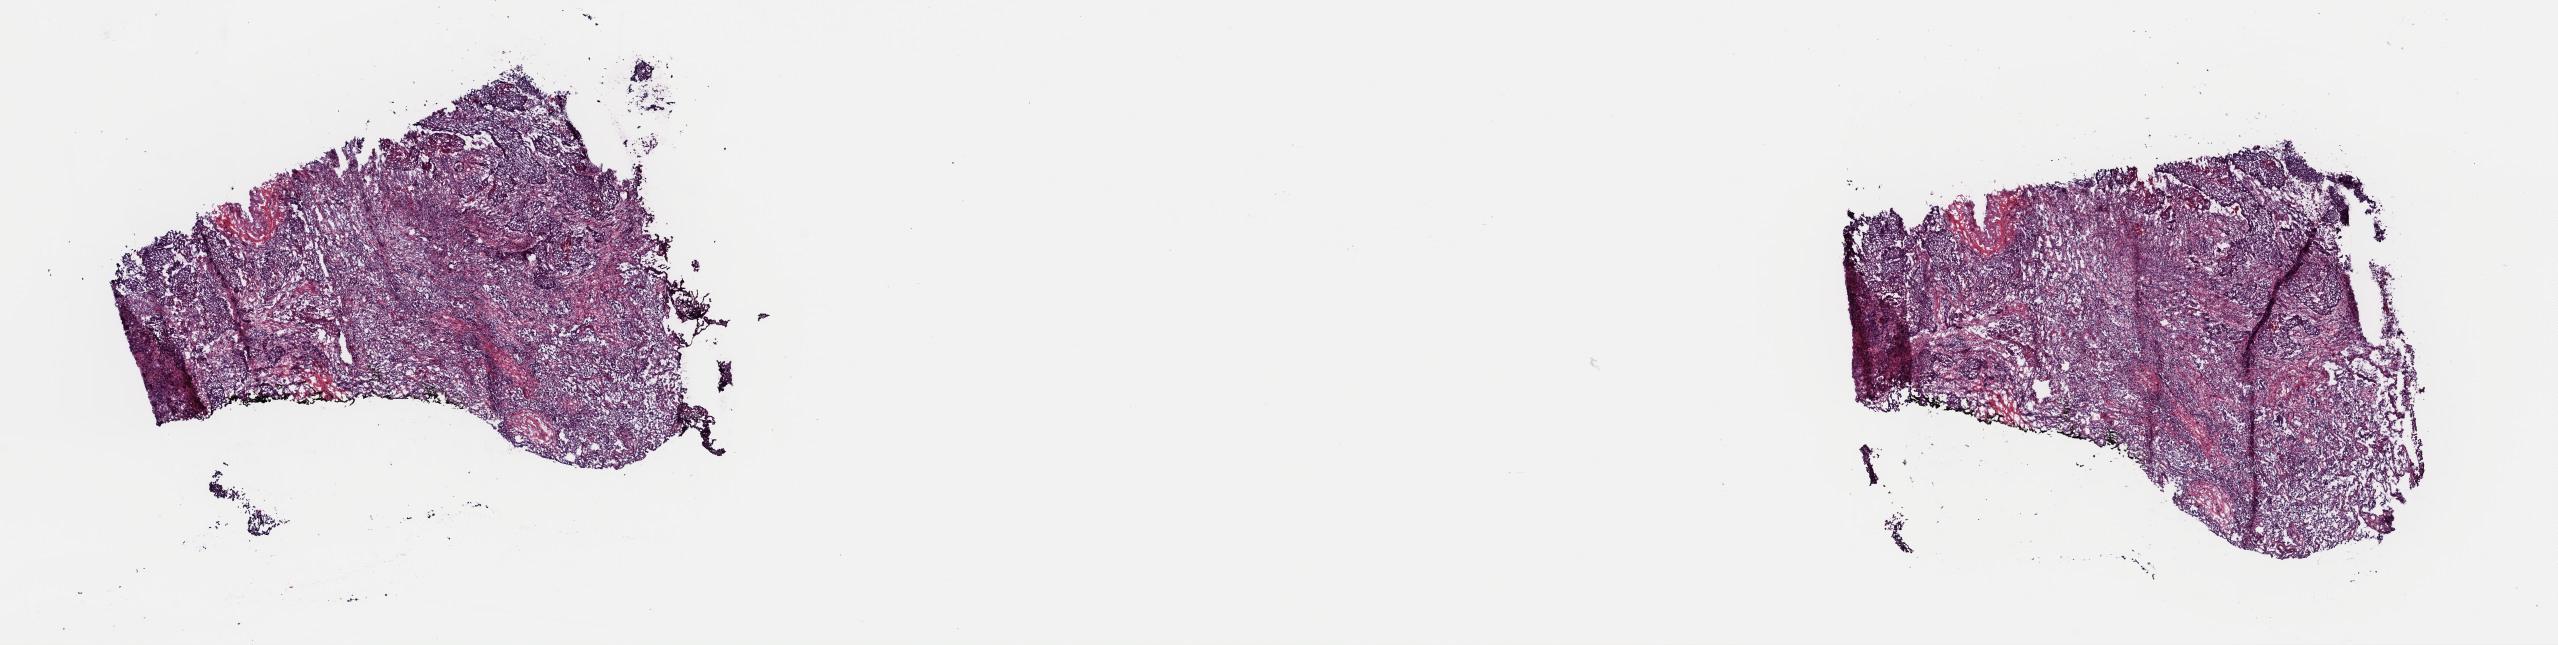
Whole-slide histology image, H&E-stained — low-resolution overview of the scanned area, about 20.2 x 5.1 mm (acquisition: 40x scan). Frozen section. Primary tumour sample from the lung. Male, age 76 years at initial diagnosis. Composition of this section per pathologist review: tumour cells 60%, tumour nuclei 70%, normal cells 0%, stromal cells 30%, necrosis 10%. Infiltration values recorded for this section: lymphocyte infiltration 0%, monocyte infiltration 0%, neutrophil infiltration 0%.
AJCC pathologic stage: IB. Diagnosis: Squamous cell carcinoma, NOS.